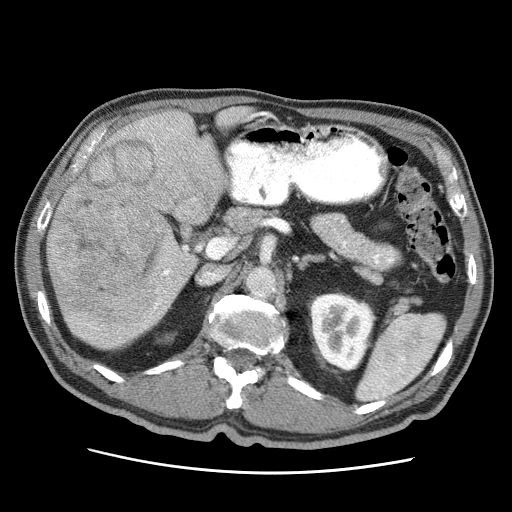
Contrast-enhanced abdominal CT (liver protocol), one axial slice. Slice 21 of 75 in the series (ordered by position). 120 kVp. Soft-tissue window (W 400 / L 40 HU). 2.5 mm slice thickness. 512 × 512 image matrix. Case-level facts recorded for this patient, not image findings: diagnosis: hepatocellular carcinoma (patient treated with transarterial chemoembolisation; whether this scan precedes or follows treatment is not stated here); TNM stage (as recorded): Stage-IIIA; Child-Pugh class: A; tumour differentiation: well differentiated; tumour nodularity: multinodular.
Outlined on this slice (semi-automatic segmentation, software-assisted and operator-edited):
- liver parenchyma outside the tumour (the mass and vessels are separate outlines, so this box may not span the whole liver): box from (x=46, y=106) to (x=258, y=348) px
- mass: (x=46, y=137)–(x=216, y=325)
- liver vessels: (x=90, y=114)–(x=256, y=330)